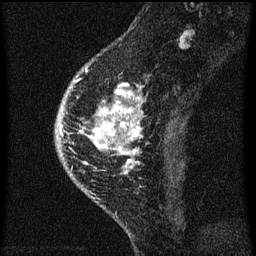
Breast MRI (dynamic contrast-enhanced), one sagittal slice. Position 21 of 60 along the scan axis. Dynamic contrast-enhanced series, image 2 of 3 at this slice position (ordered by acquisition). 1.5 T. TE 4.2 ms, TR 8 ms. 256 × 256 image matrix. Female patient, age 46 years.
Outlined on this slice (semi-automatic segmentation, software-assisted and operator-edited):
- analysis volume of interest (the breast-tissue region the enhancement analysis was run in; not a lesion): box from (x=82, y=68) to (x=145, y=195) px
- tumour enhancement mask (voxels above the 70 % enhancement threshold inside the analysis volume of interest): (x=83, y=68)–(x=143, y=175)